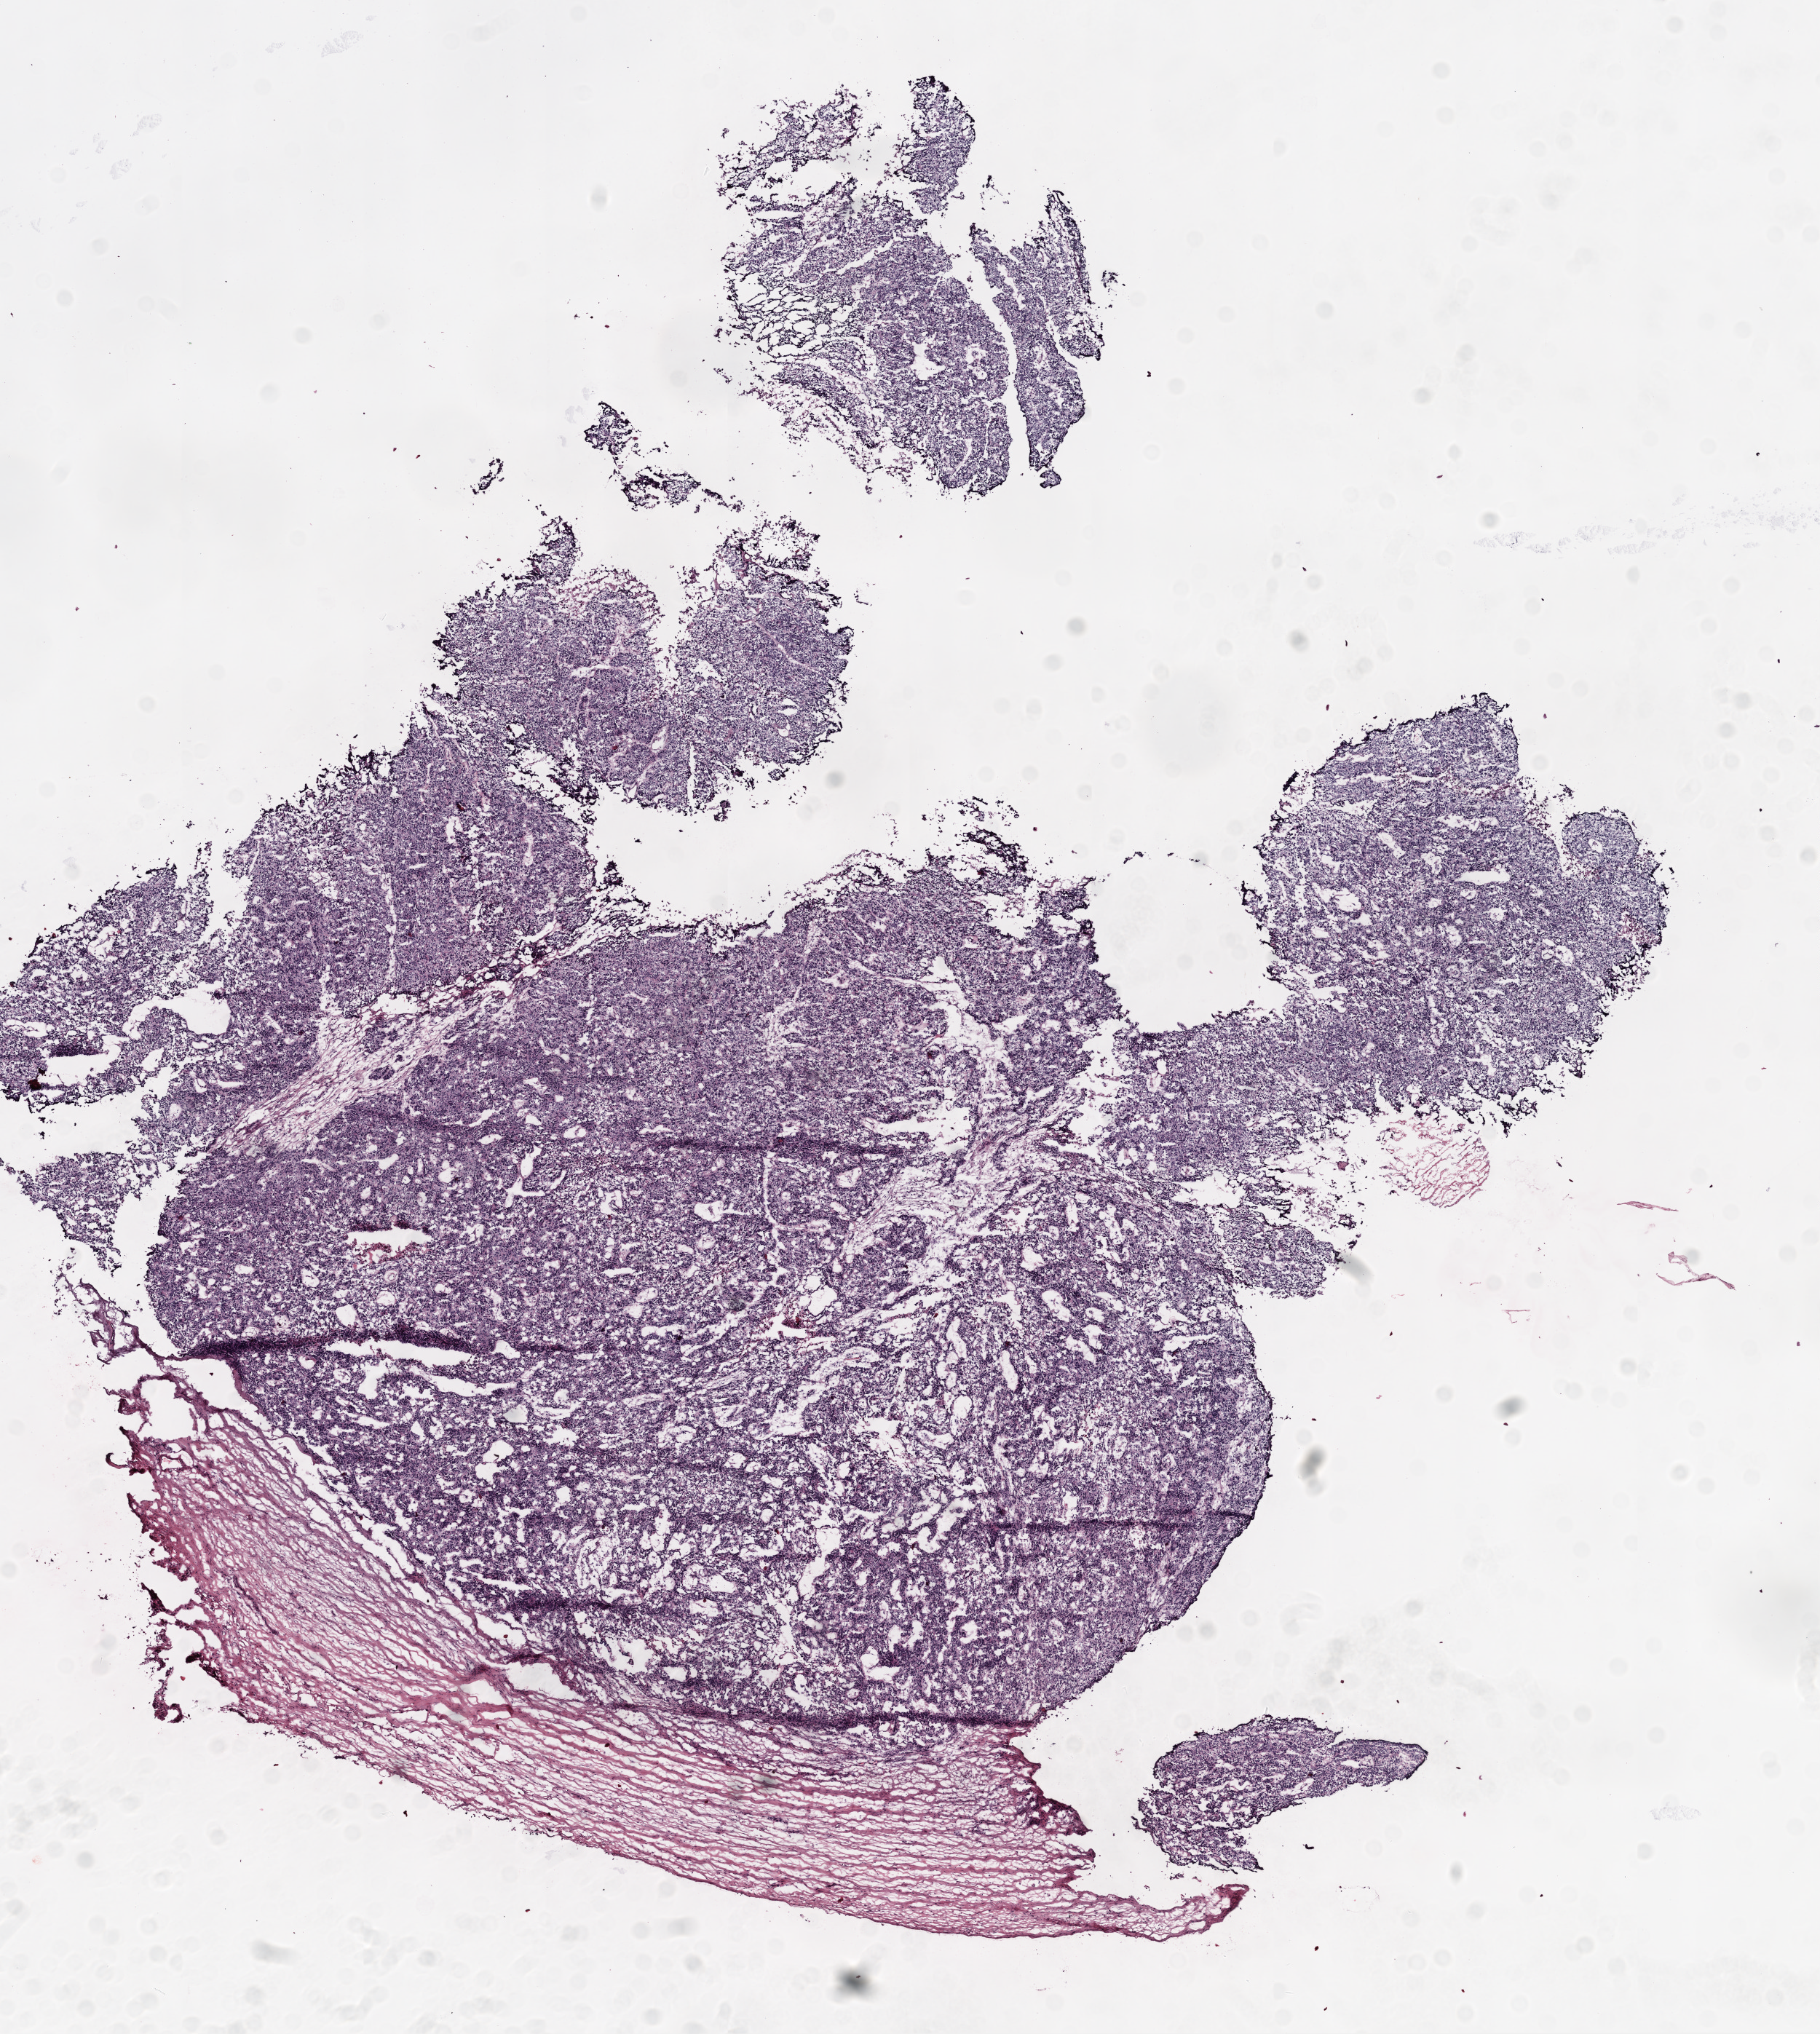
Whole-slide histology image, H&E — a low-resolution overview of the entire scanned area, about 10.0 x 11.2 mm (slide scanned at 20x). Frozen section from the top of the tissue portion. Ovary, primary tumour sample. Patient: female, age at initial diagnosis 60 years. Composition of this section per pathologist review: tumour cells 80%, tumour nuclei 97%.
Diagnosis: Serous cystadenocarcinoma, NOS.